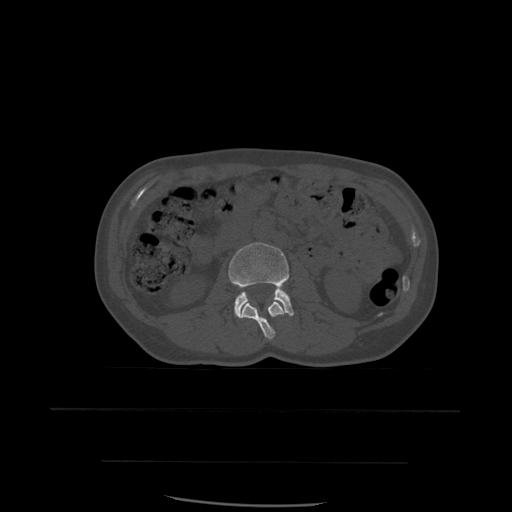
CT including the spine, one axial slice; position 209 of 574 along the scan axis; bone window (W 1800 / L 400 HU); 512 × 512 image matrix, field of view 392 × 392 mm. Patient age 48 years. From the clinical record (not read from this slice): primary cancer: lung.
Structures marked on this image (semi-automatically segmented with operator editing):
- L2 vertebra: bounding box <239,302,284,340> (left, top, right, bottom; pixels)
- L3 vertebra: <229,243,294,318>